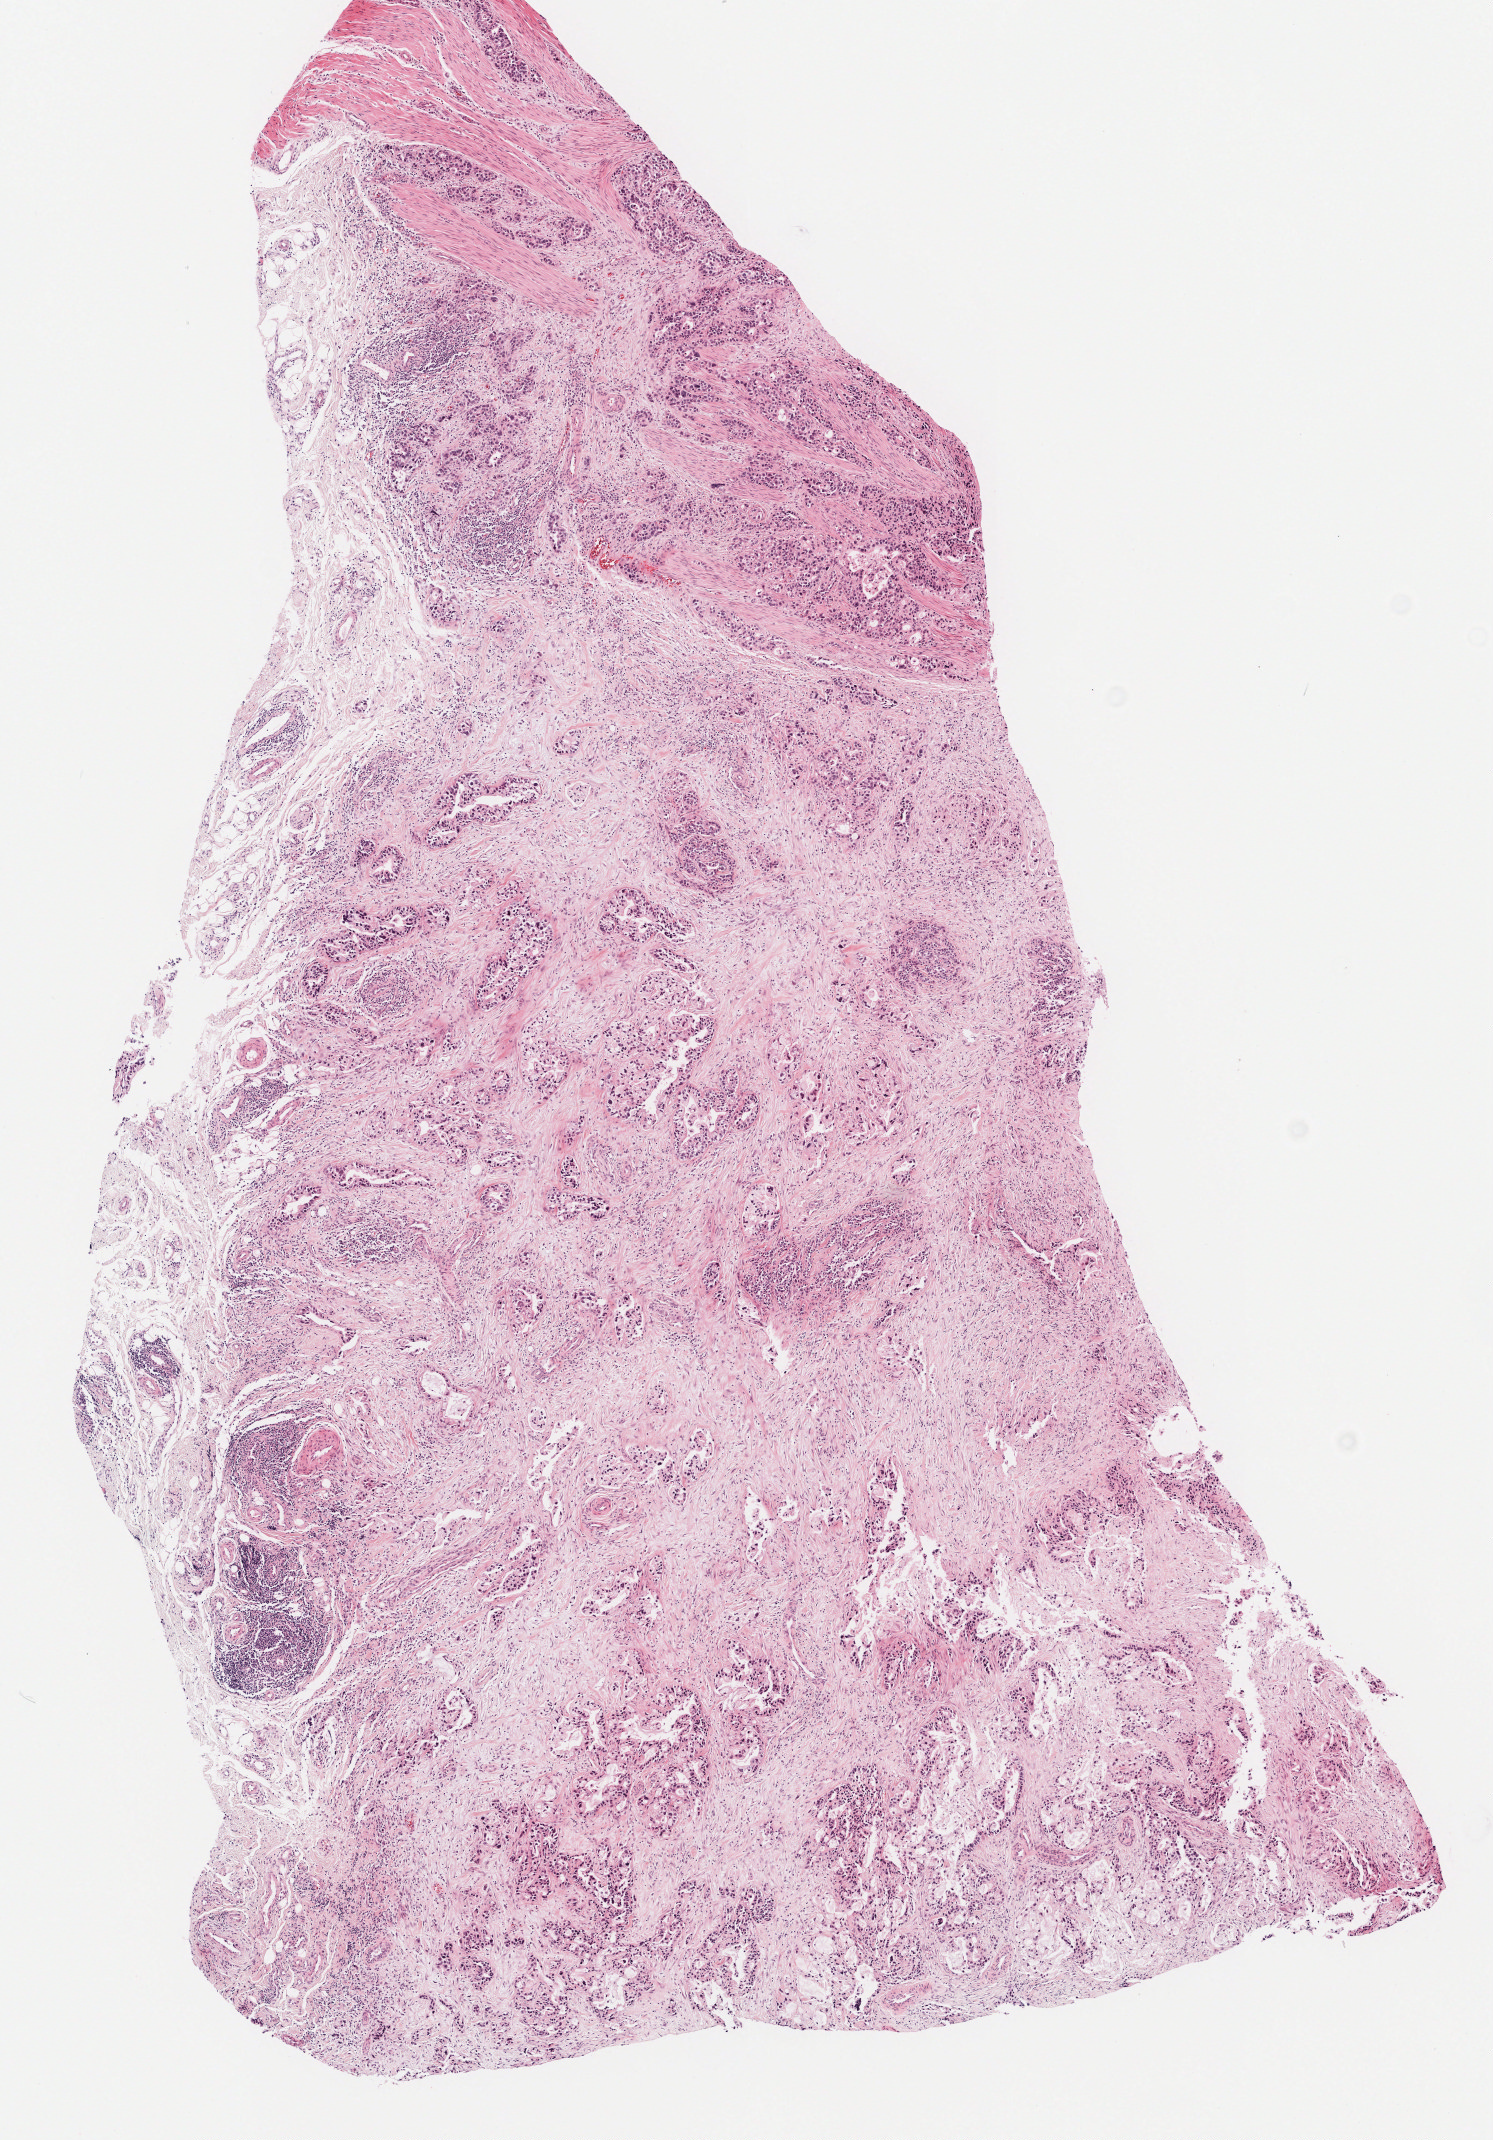
H&E whole-slide image — shown as a low-resolution overview of the whole scanned area (about 5.9 x 8.5 mm, slide scanned at 20x). Formalin-fixed paraffin-embedded (FFPE) diagnostic section. Primary tumour sample from the stomach. Patient: male, age at initial diagnosis 74 years. Histologic grade: G3 (poorly differentiated).
* AJCC pathologic stage: IIIB
* pathologic diagnosis: Carcinoma, diffuse type (gastric antrum)
* lymph nodes positive (case pathology): 3 of 29 examined